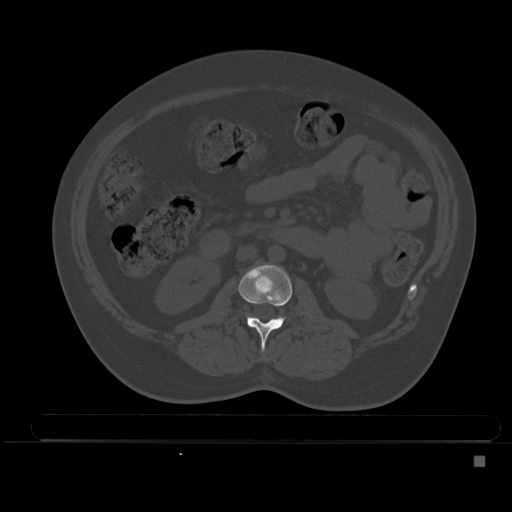
CT including the spine, one axial slice; position 169 of 495 along the scan axis; bone window (W 1800 / L 400 HU); 512 × 512 image matrix. Patient: female, 33 years. From the clinical record (not read from this slice): primary cancer: breast; vertebrae with lytic lesions (as recorded): T1.
Structures marked on this image (semi-automatically segmented with operator editing):
- L2 vertebra: box from (x=239, y=264) to (x=292, y=350) px